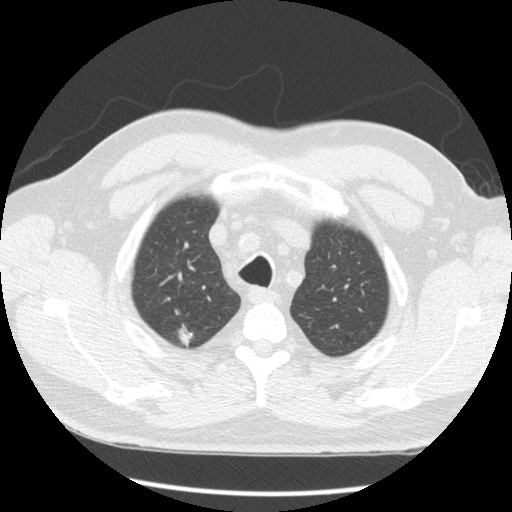
Low-dose screening chest CT, axial slice, baseline screening round, lung window (W 1500 / L -600 HU), 2.5 mm slice thickness, 512 × 512 image matrix, field of view 360 × 360 mm. Male participant, aged 65 years at enrolment. Former smoker at enrolment.
• Lesion marked by an expert reader, bounding box (x1, y1, x2, y2) in pixels: (160, 320, 206, 359).
• The exam's reader record, not a measurement of the box and not confirmed to be the same lesion: non-calcified nodule or mass ≥4 mm, right upper lobe, 10 × 9 mm, spiculated (stellate) margins, soft tissue attenuation.
• Official screen result: positive, change unspecified: nodule(s) >= 4 mm or enlarging nodule(s), mass(es), or other non-specific abnormalities suspicious for lung cancer.
• Later outcome: lung cancer diagnosed 103 days after this screen — squamous cell carcinoma, NOS, right upper lobe, poorly differentiated (G3), stage IA (AJCC 6th edition), 5 mm at pathology.